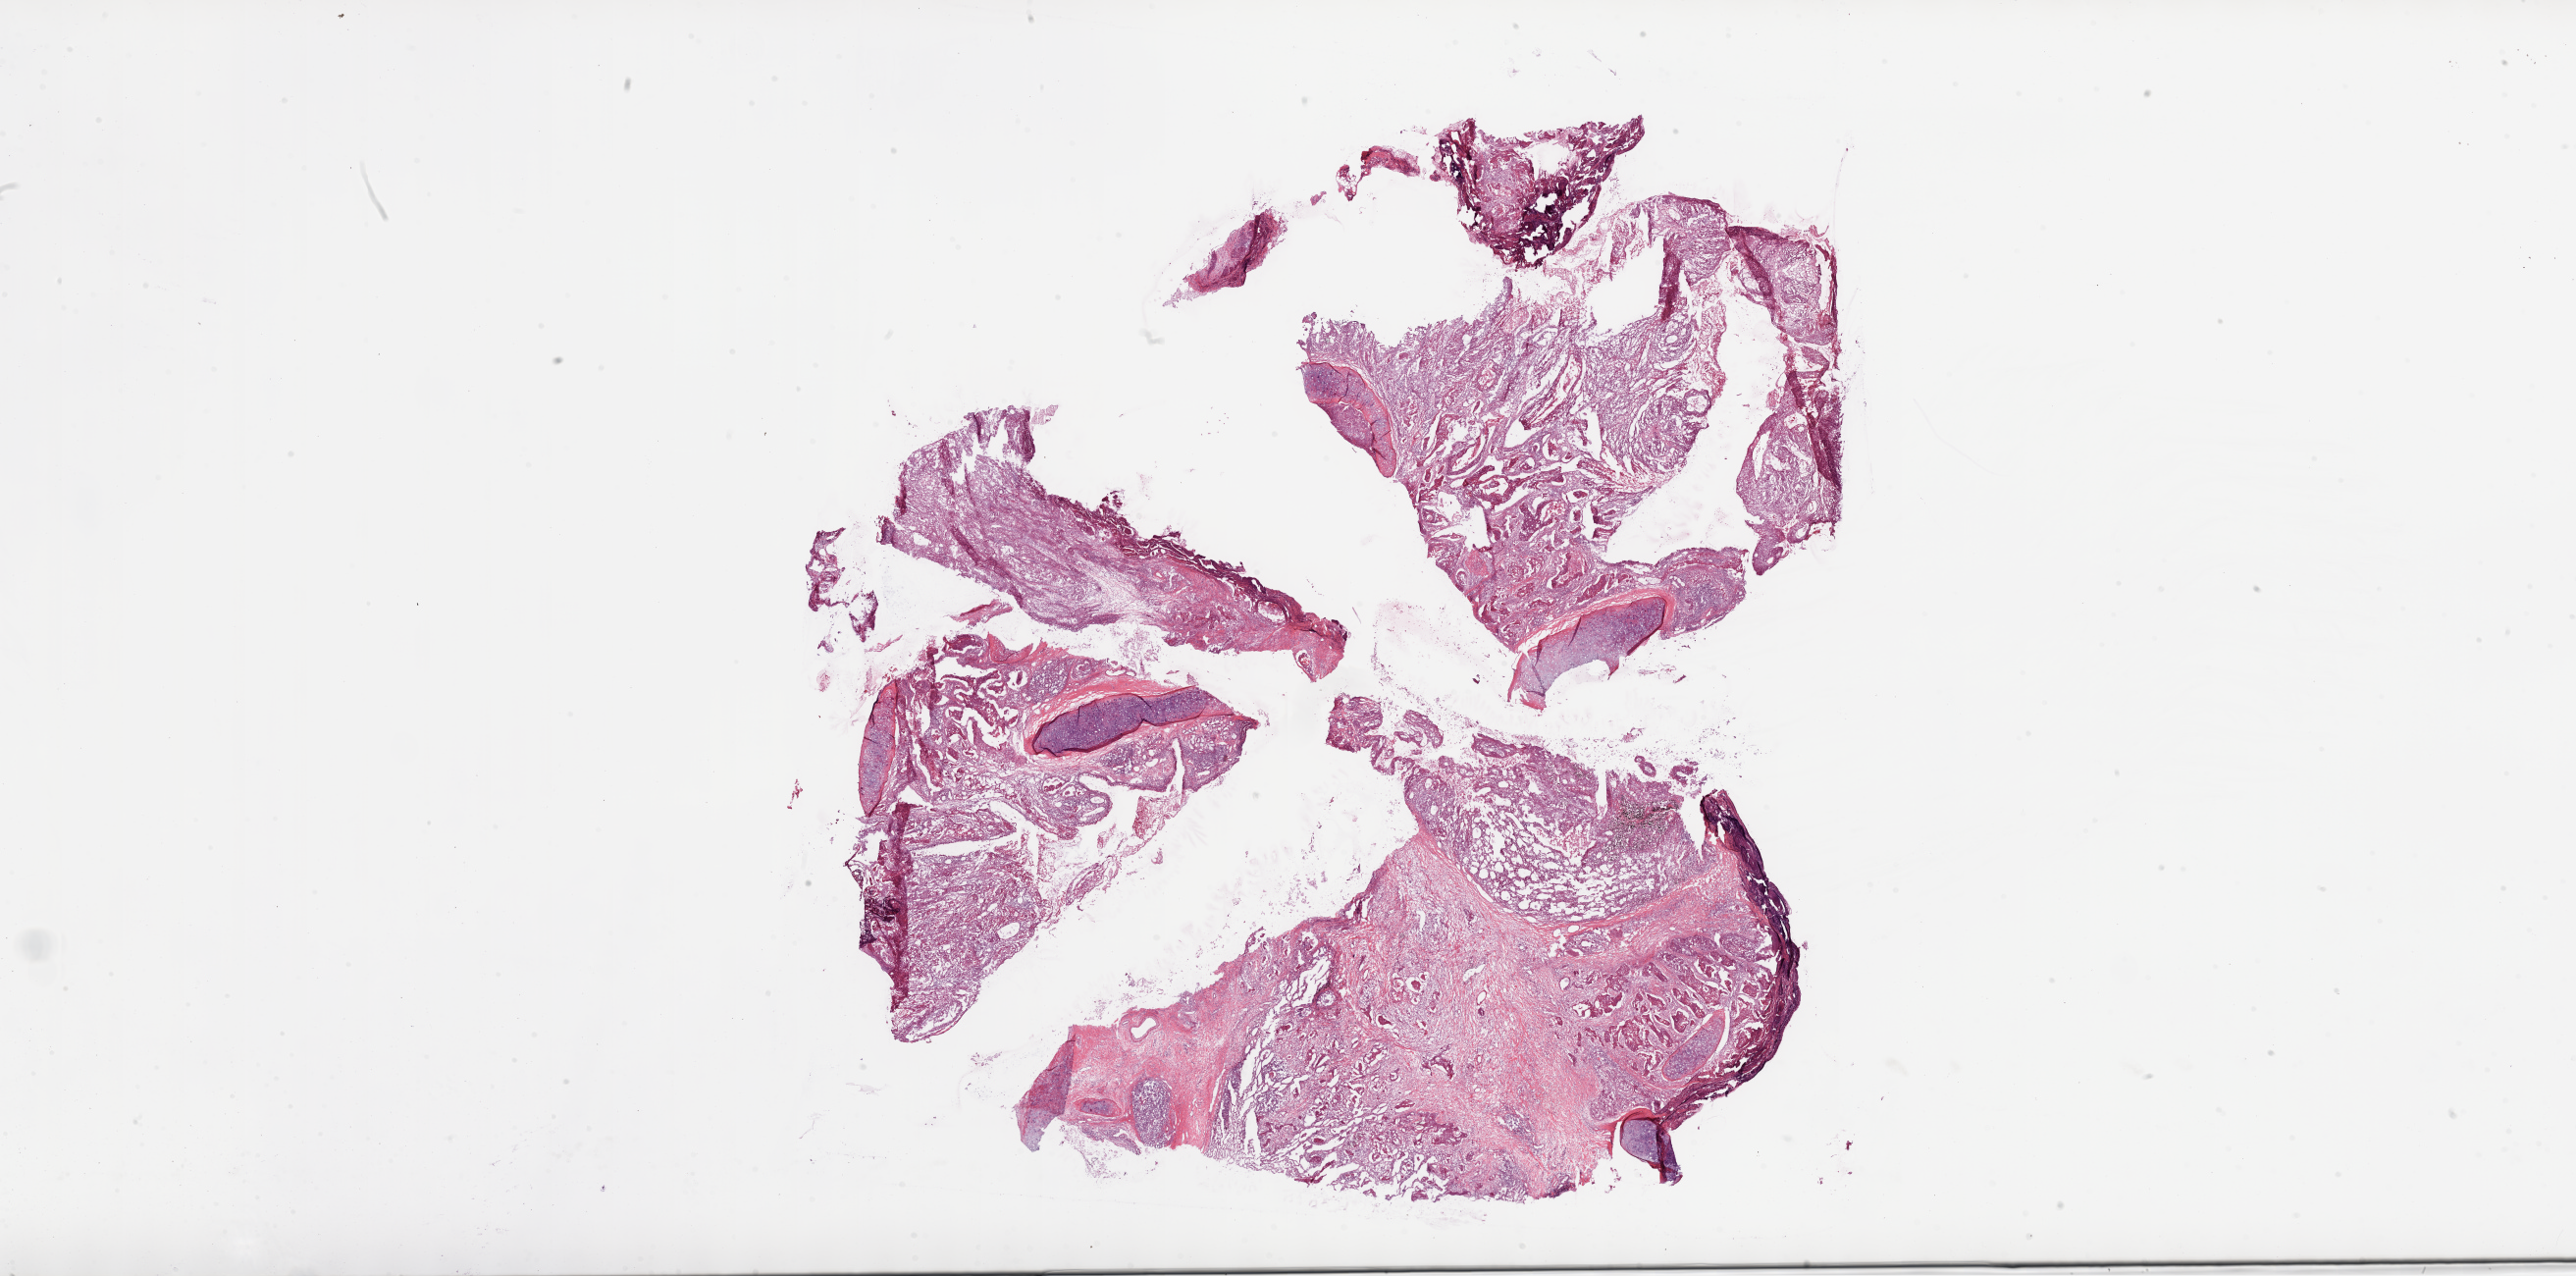
Whole-slide histology image, H&E — a low-resolution overview of the entire scanned area, about 42.1 x 20.9 mm; frozen section; sample: primary tumour, lung. Patient: female, age at initial diagnosis 65 years. Pathologist review of this section (percent, as recorded): tumour cells 70%, tumour nuclei 70%, normal cells 5%, stromal cells 20%, necrosis 5%. Inflammatory infiltration, as recorded: lymphocyte infiltration 15%, monocyte infiltration 2%, neutrophil infiltration 2%.
TNM: T2a N2 M0. Histologic diagnosis: Squamous cell carcinoma, NOS. AJCC pathologic stage: IIIA (7th edition).